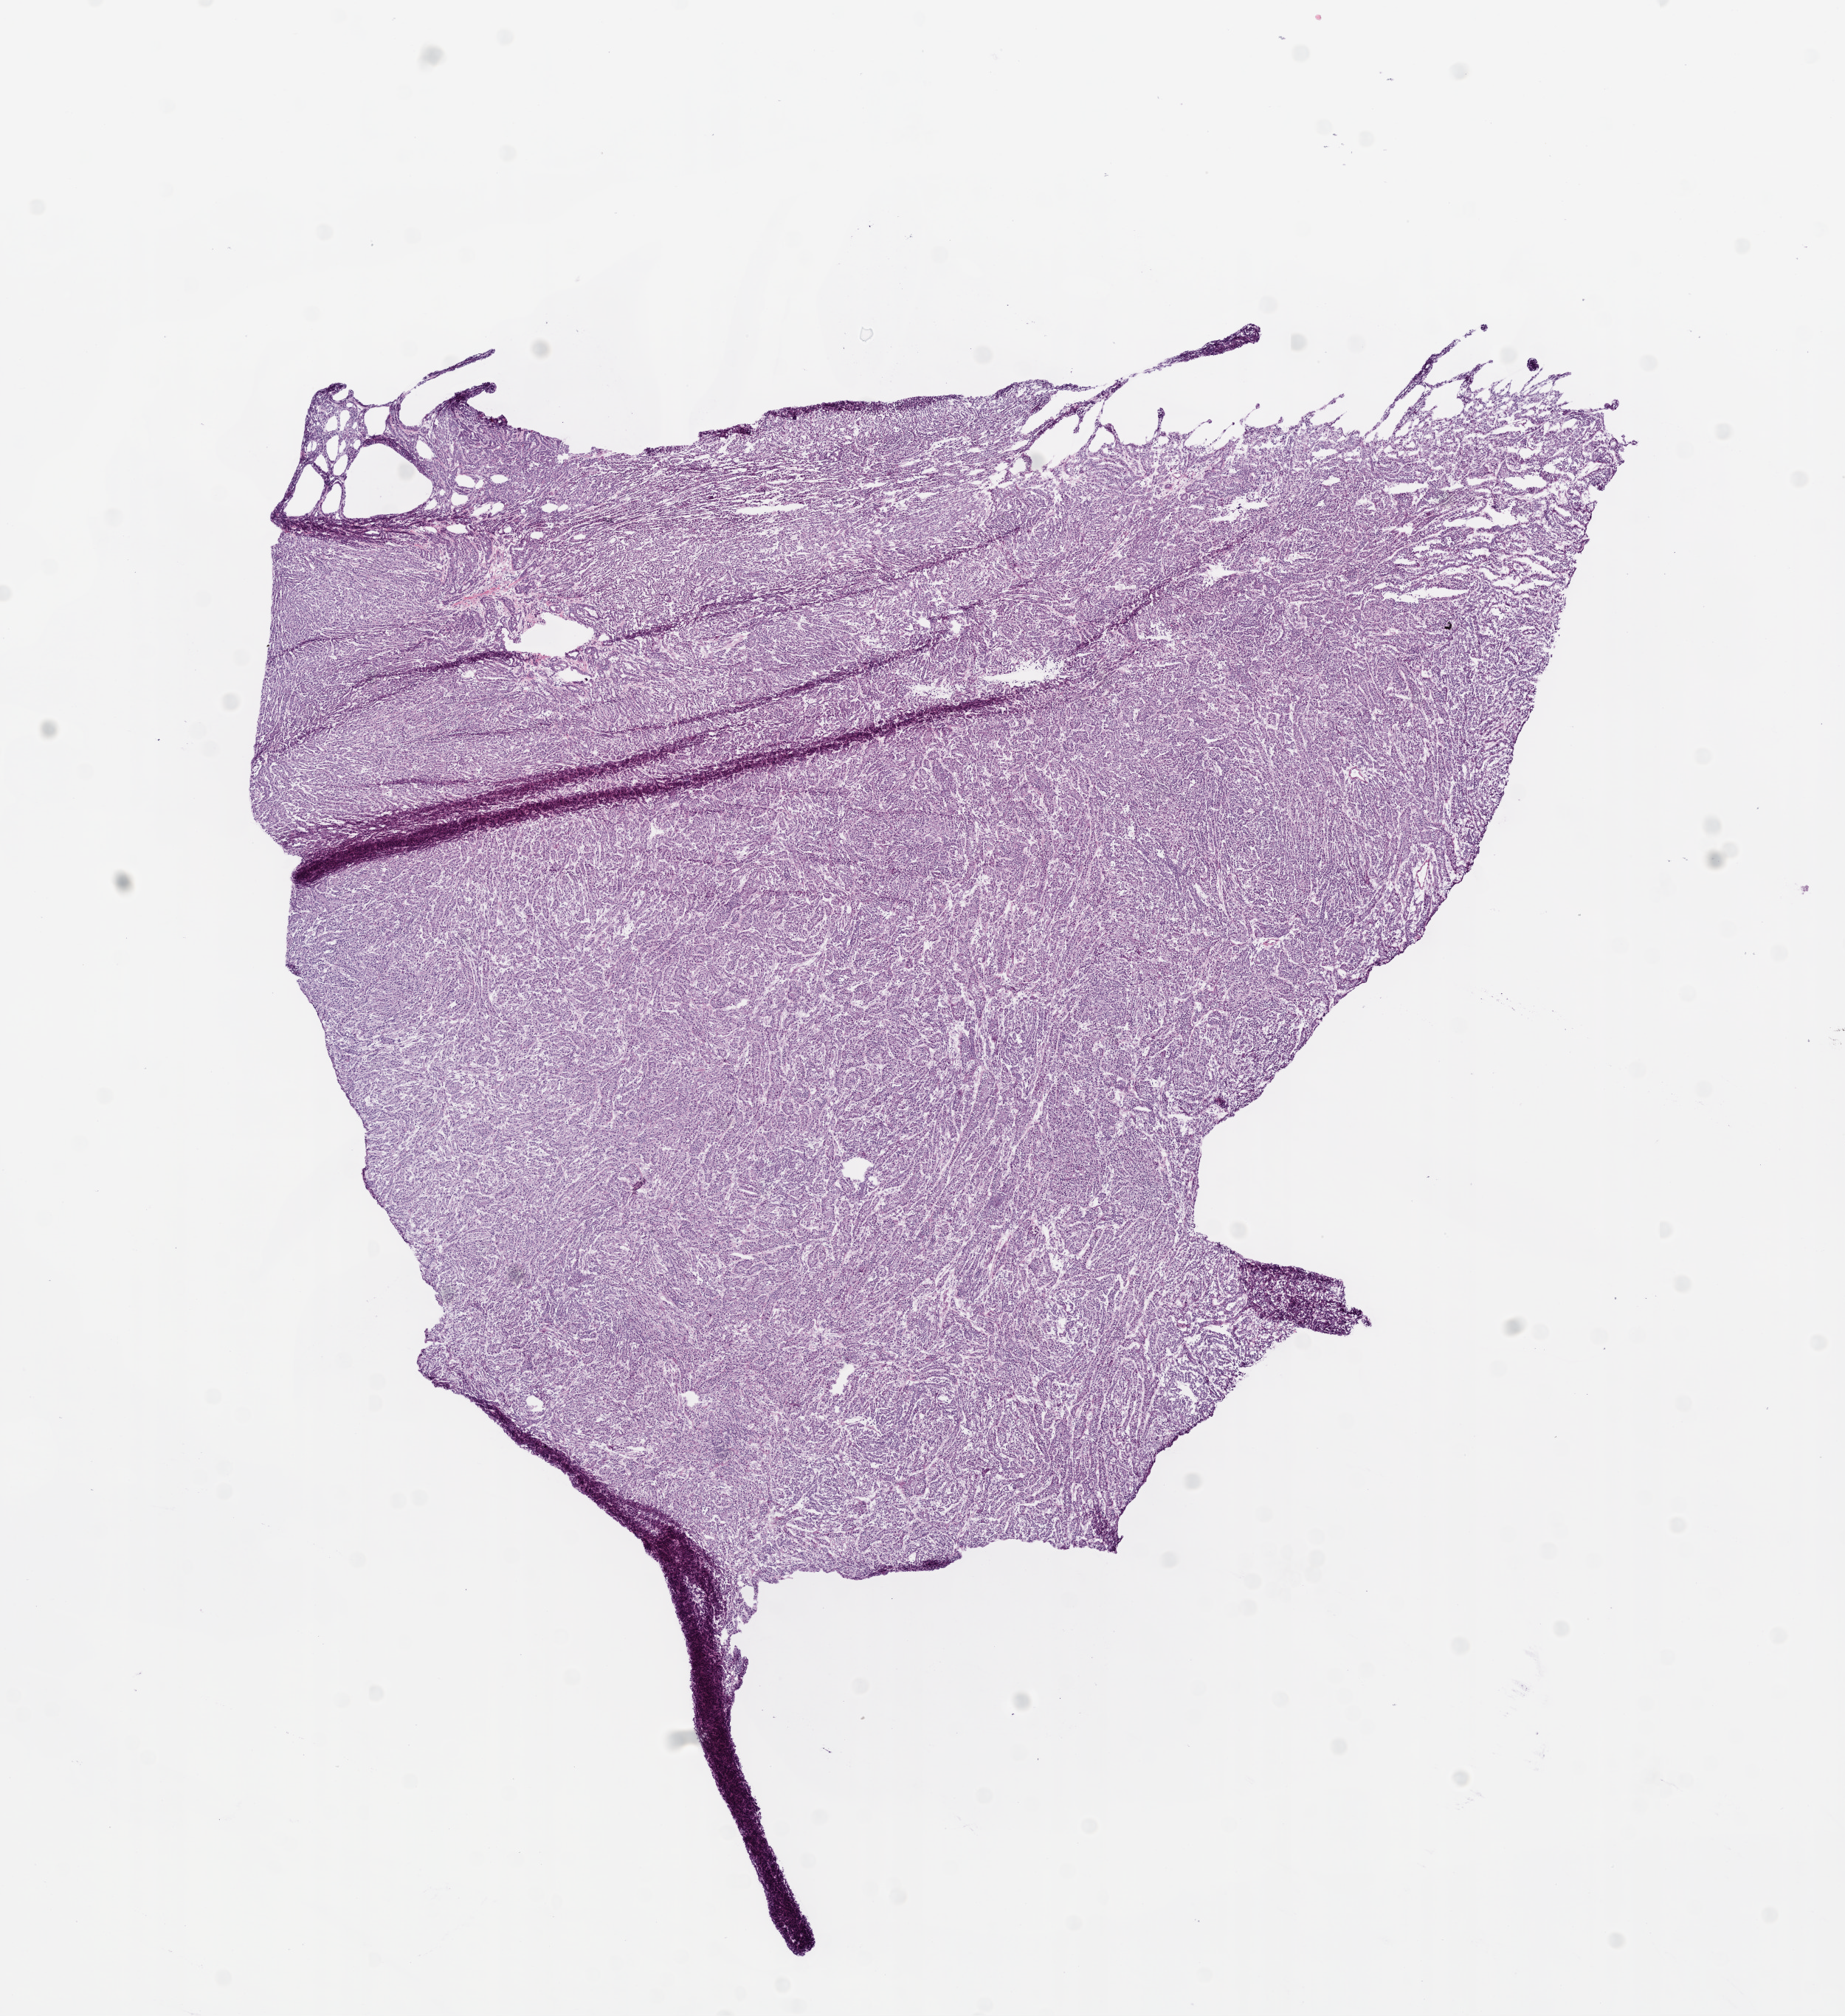
Whole-slide histology image, H&E-stained, shown as a low-resolution overview of the whole scanned area (about 10.0 x 11.0 mm); frozen section; kidney, primary tumour sample. Patient: female, age at initial diagnosis 59 years. Composition of this section per pathologist review: tumour cells 98%, tumour nuclei 90%, normal cells 0%, stromal cells 2%, necrosis 0%.
- TNM: T1 NX M0
- laterality: left
- diagnosis: Papillary adenocarcinoma, NOS
- AJCC pathologic stage: I